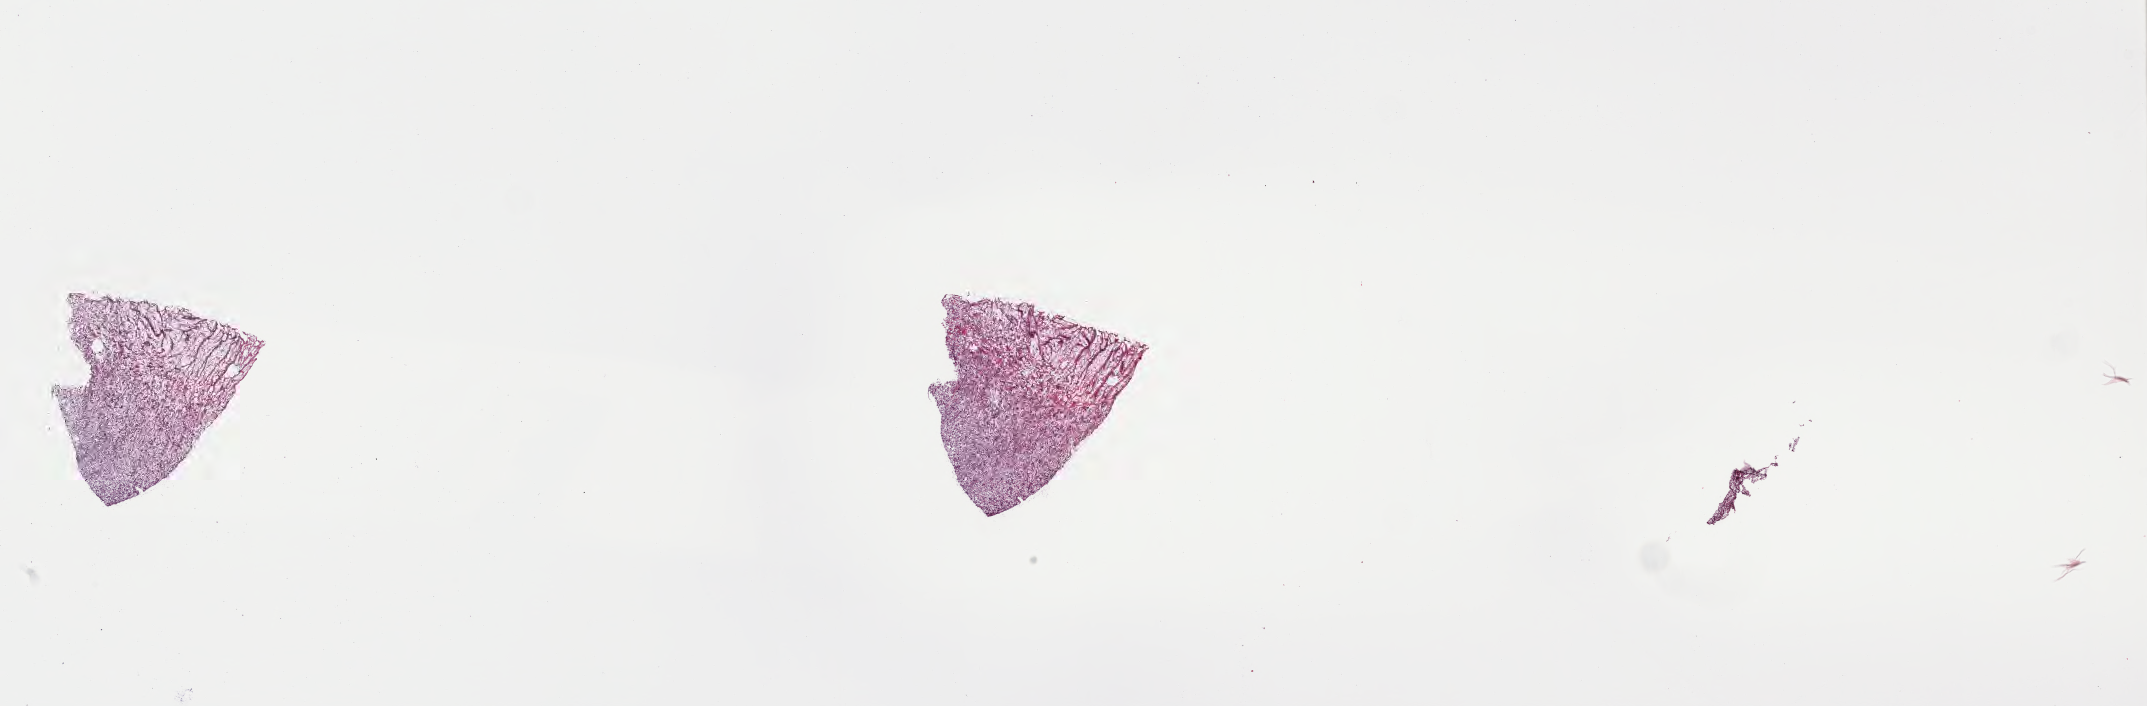
Digitized H&E-stained section of tumor tissue from the soft tissue of pelvis — shown as a low-resolution overview of the whole scanned area (about 34.7 x 11.4 mm). Cryosection (OCT / tissue freezing medium). Male patient, age 179 months (14 years 11 months).
• tissue or organ of origin (case record): connective, subcutaneous and other soft tissues of pelvis
• diagnosis (ICD-O-3 morphology term): Rhabdomyosarcoma, NOS